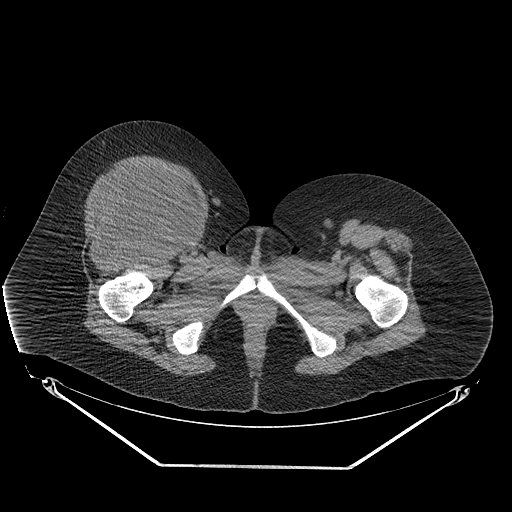
CT of an extremity soft-tissue mass (from a PET/CT study), one axial slice; position 56 of 267 along the scan axis; reconstruction kernel STANDARD; 140 kVp; soft-tissue window (W 400 / L 40 HU); 3.75 mm slice thickness; 512 × 512 image matrix, field of view 500 × 500 mm. Female patient. From the clinical record (not read from this slice): histological type: malignant solitary fibrous tumor; grade: intermediate; site of the primary tumour: right thigh.
Outlined on this slice (expert contour drawn on MRI and transferred to this co-registered scan by the dataset authors):
- gross tumour volume including surrounding oedema: box from (x=87, y=165) to (x=195, y=241) px
- gross tumour volume (mass): (x=87, y=167)–(x=191, y=241)